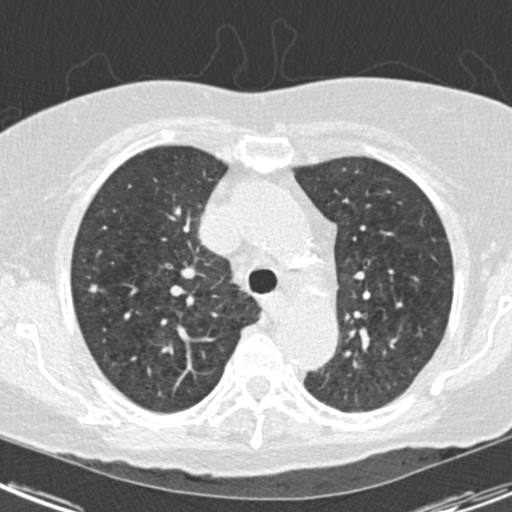
Low-dose screening chest CT, one axial slice; position 118 of 163 along the scan axis; reconstruction kernel B30f; lung window (W 1500 / L -600 HU); 512 × 512 image matrix, field of view 293 × 293 mm.
Outlined on this slice (expert manual segmentation):
- lesion 1 (tumor, upper lobe of right lung): bounding box <89,284,98,293> (left, top, right, bottom; pixels)